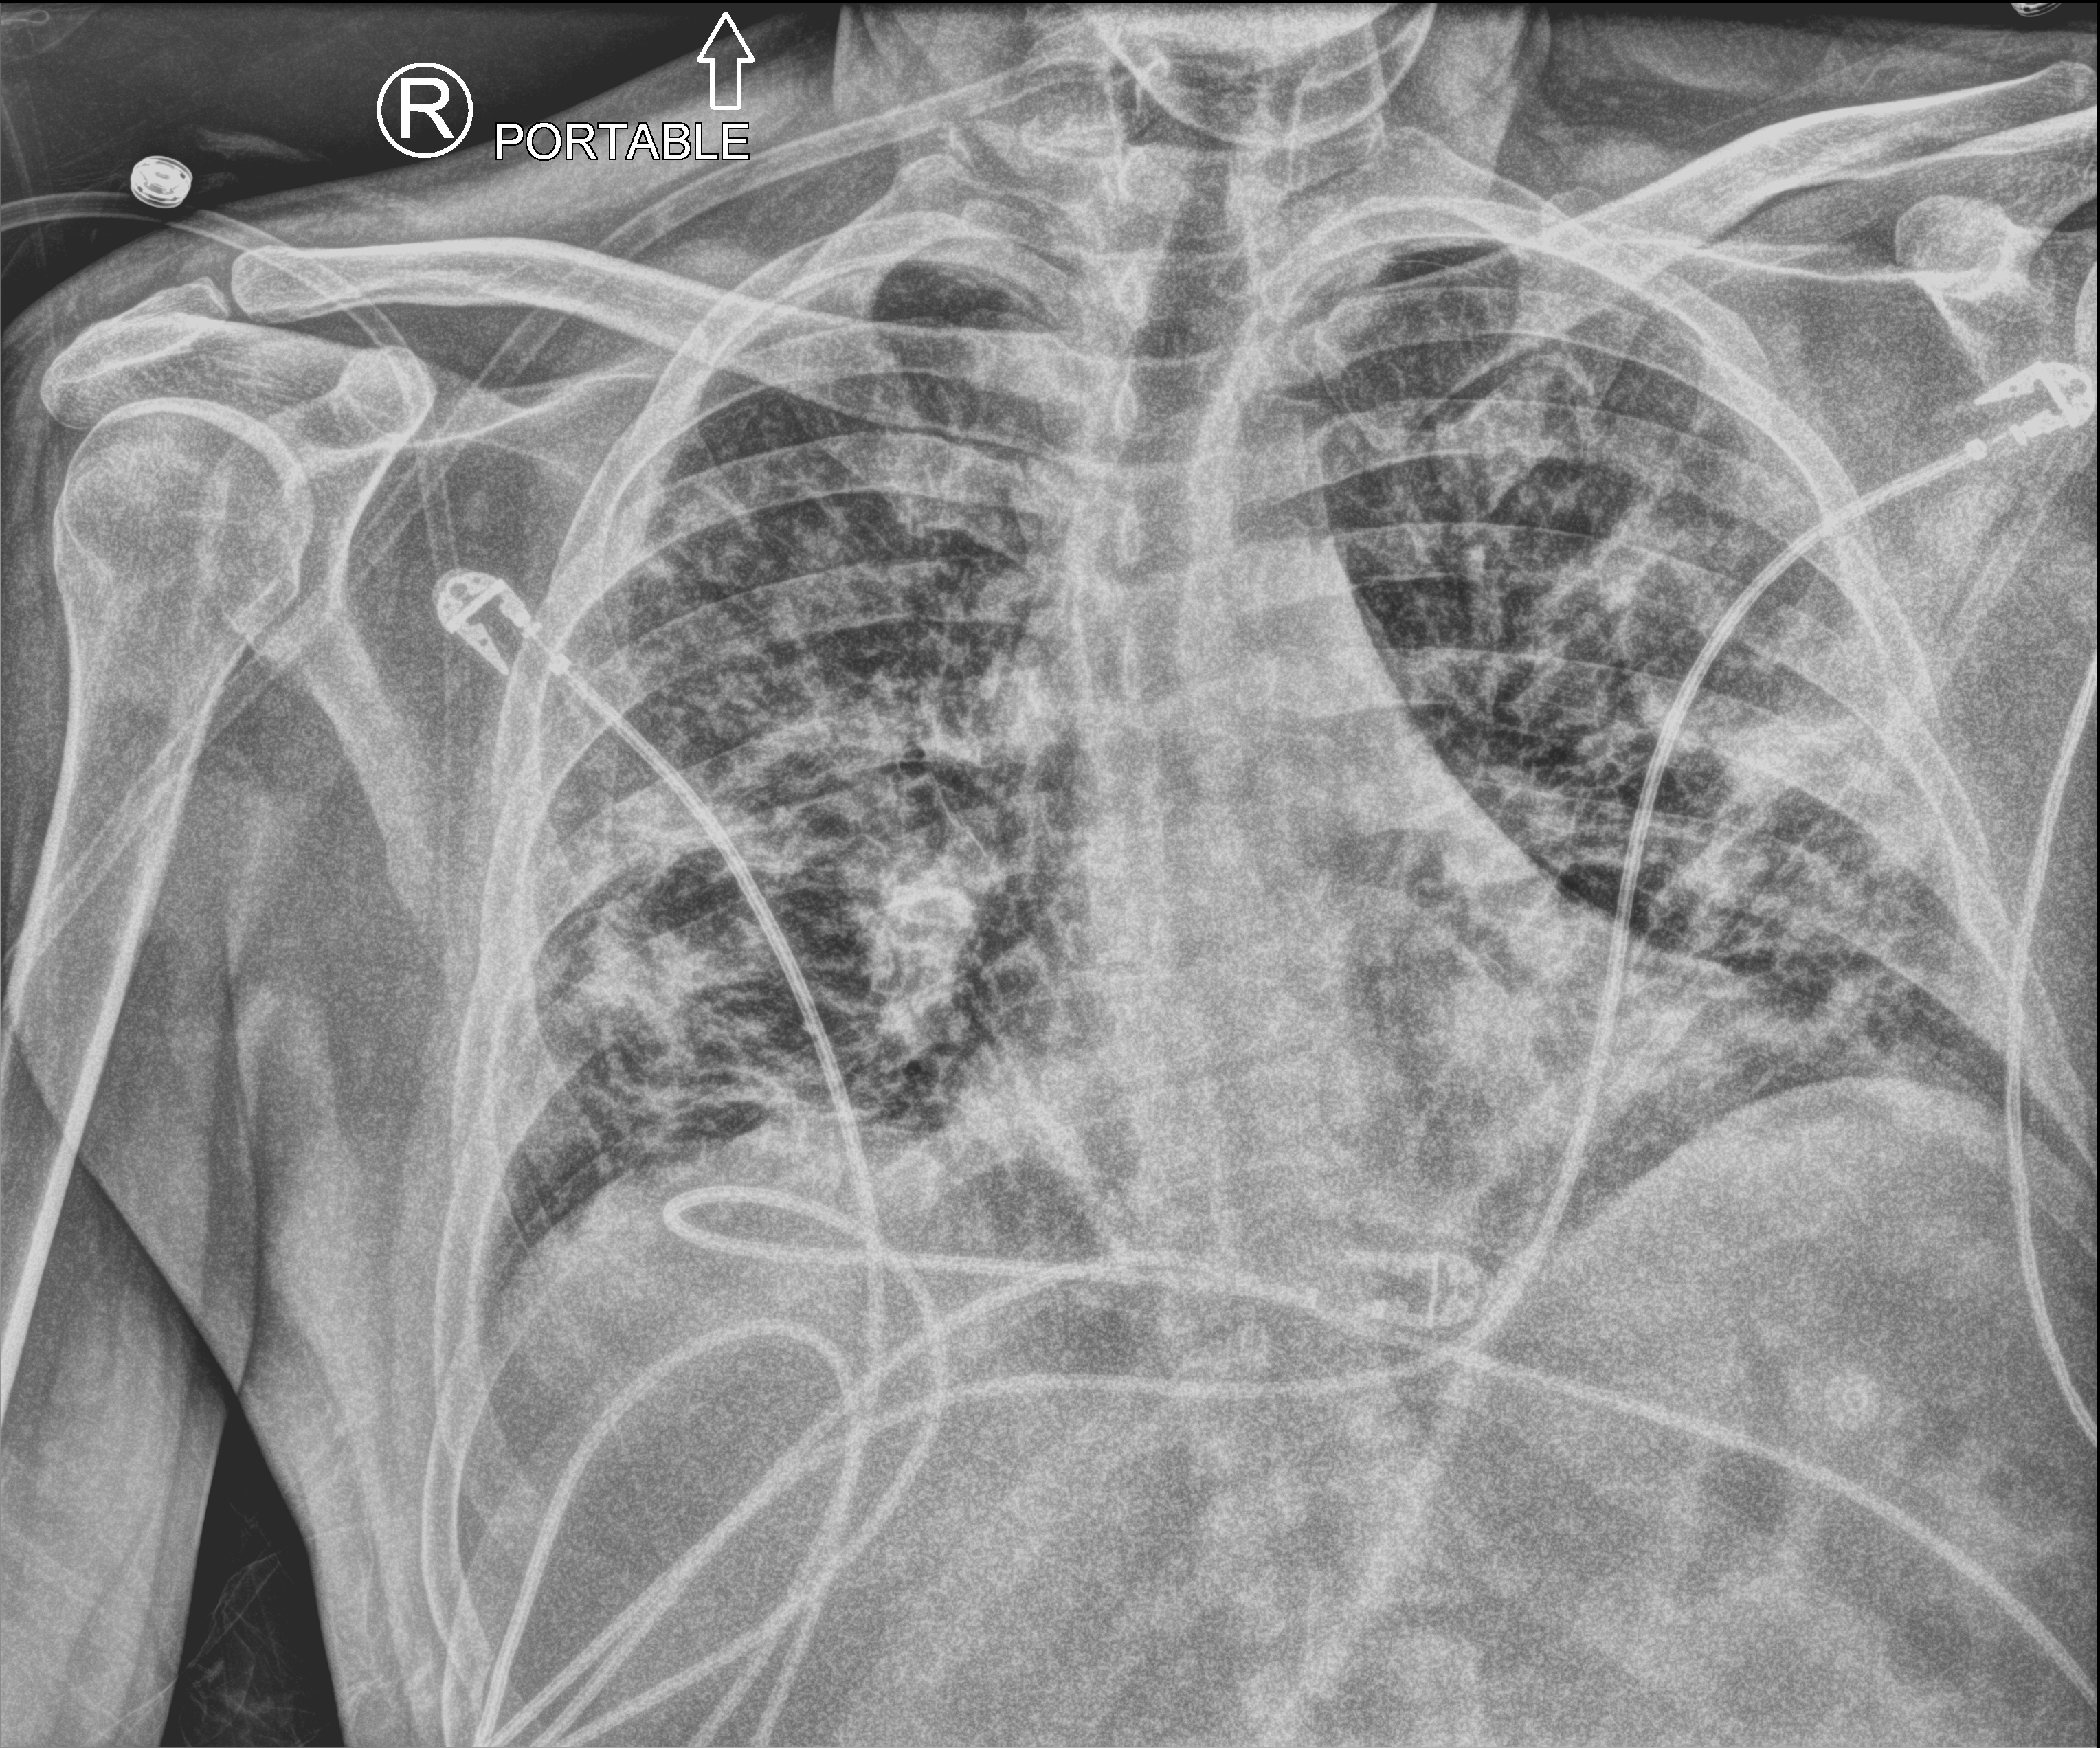
Portable chest radiograph; anteroposterior (AP) projection. Patient hospitalised with COVID-19; male, aged 60–74 years.
Admission-level facts for this patient (not findings on this image; timing relative to this image not recorded): admitted to intensive care during this hospital stay: no.